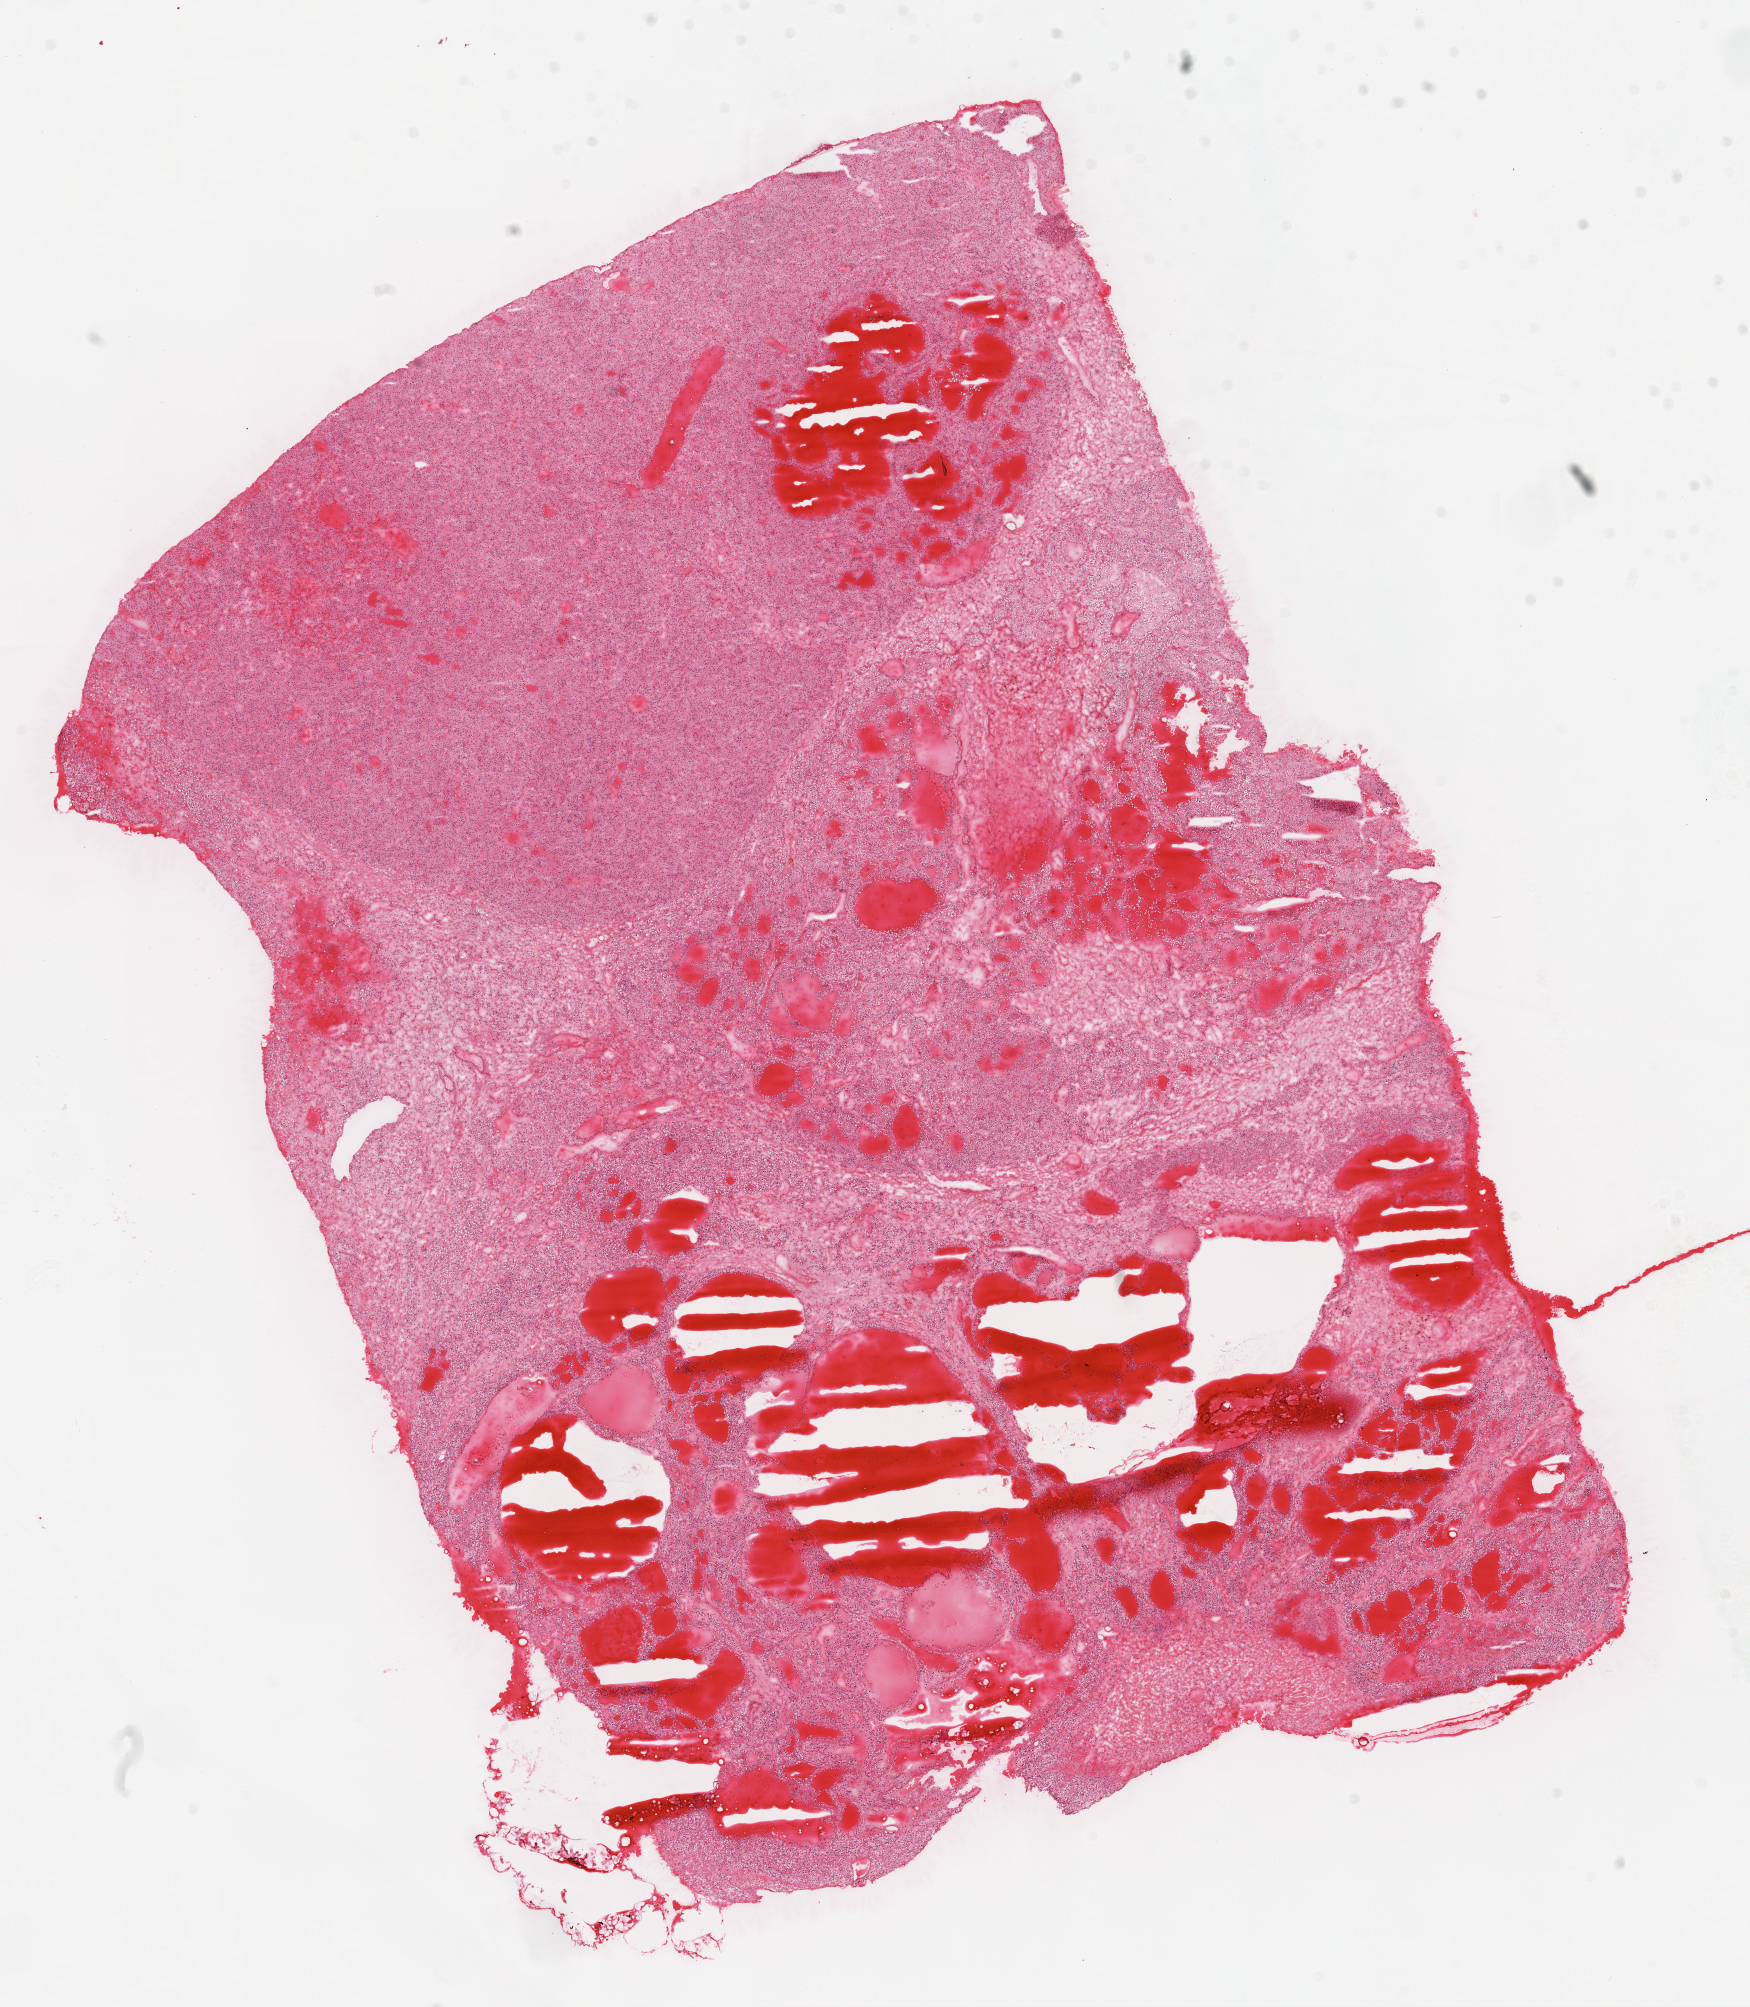
Digitized H&E-stained tissue section (whole slide), shown as a low-resolution overview of the whole scanned area (about 14.0 x 16.1 mm). Frozen section. Kidney, primary tumour sample. Male, age 52 years at initial diagnosis. Histologic grade: G2 (moderately differentiated). Composition of this section per pathologist review: tumour cells 90%, tumour nuclei 90%, normal cells 0%, stromal cells 10%, necrosis 0%.
- diagnosis: Clear cell adenocarcinoma, NOS
- AJCC pathologic stage: I